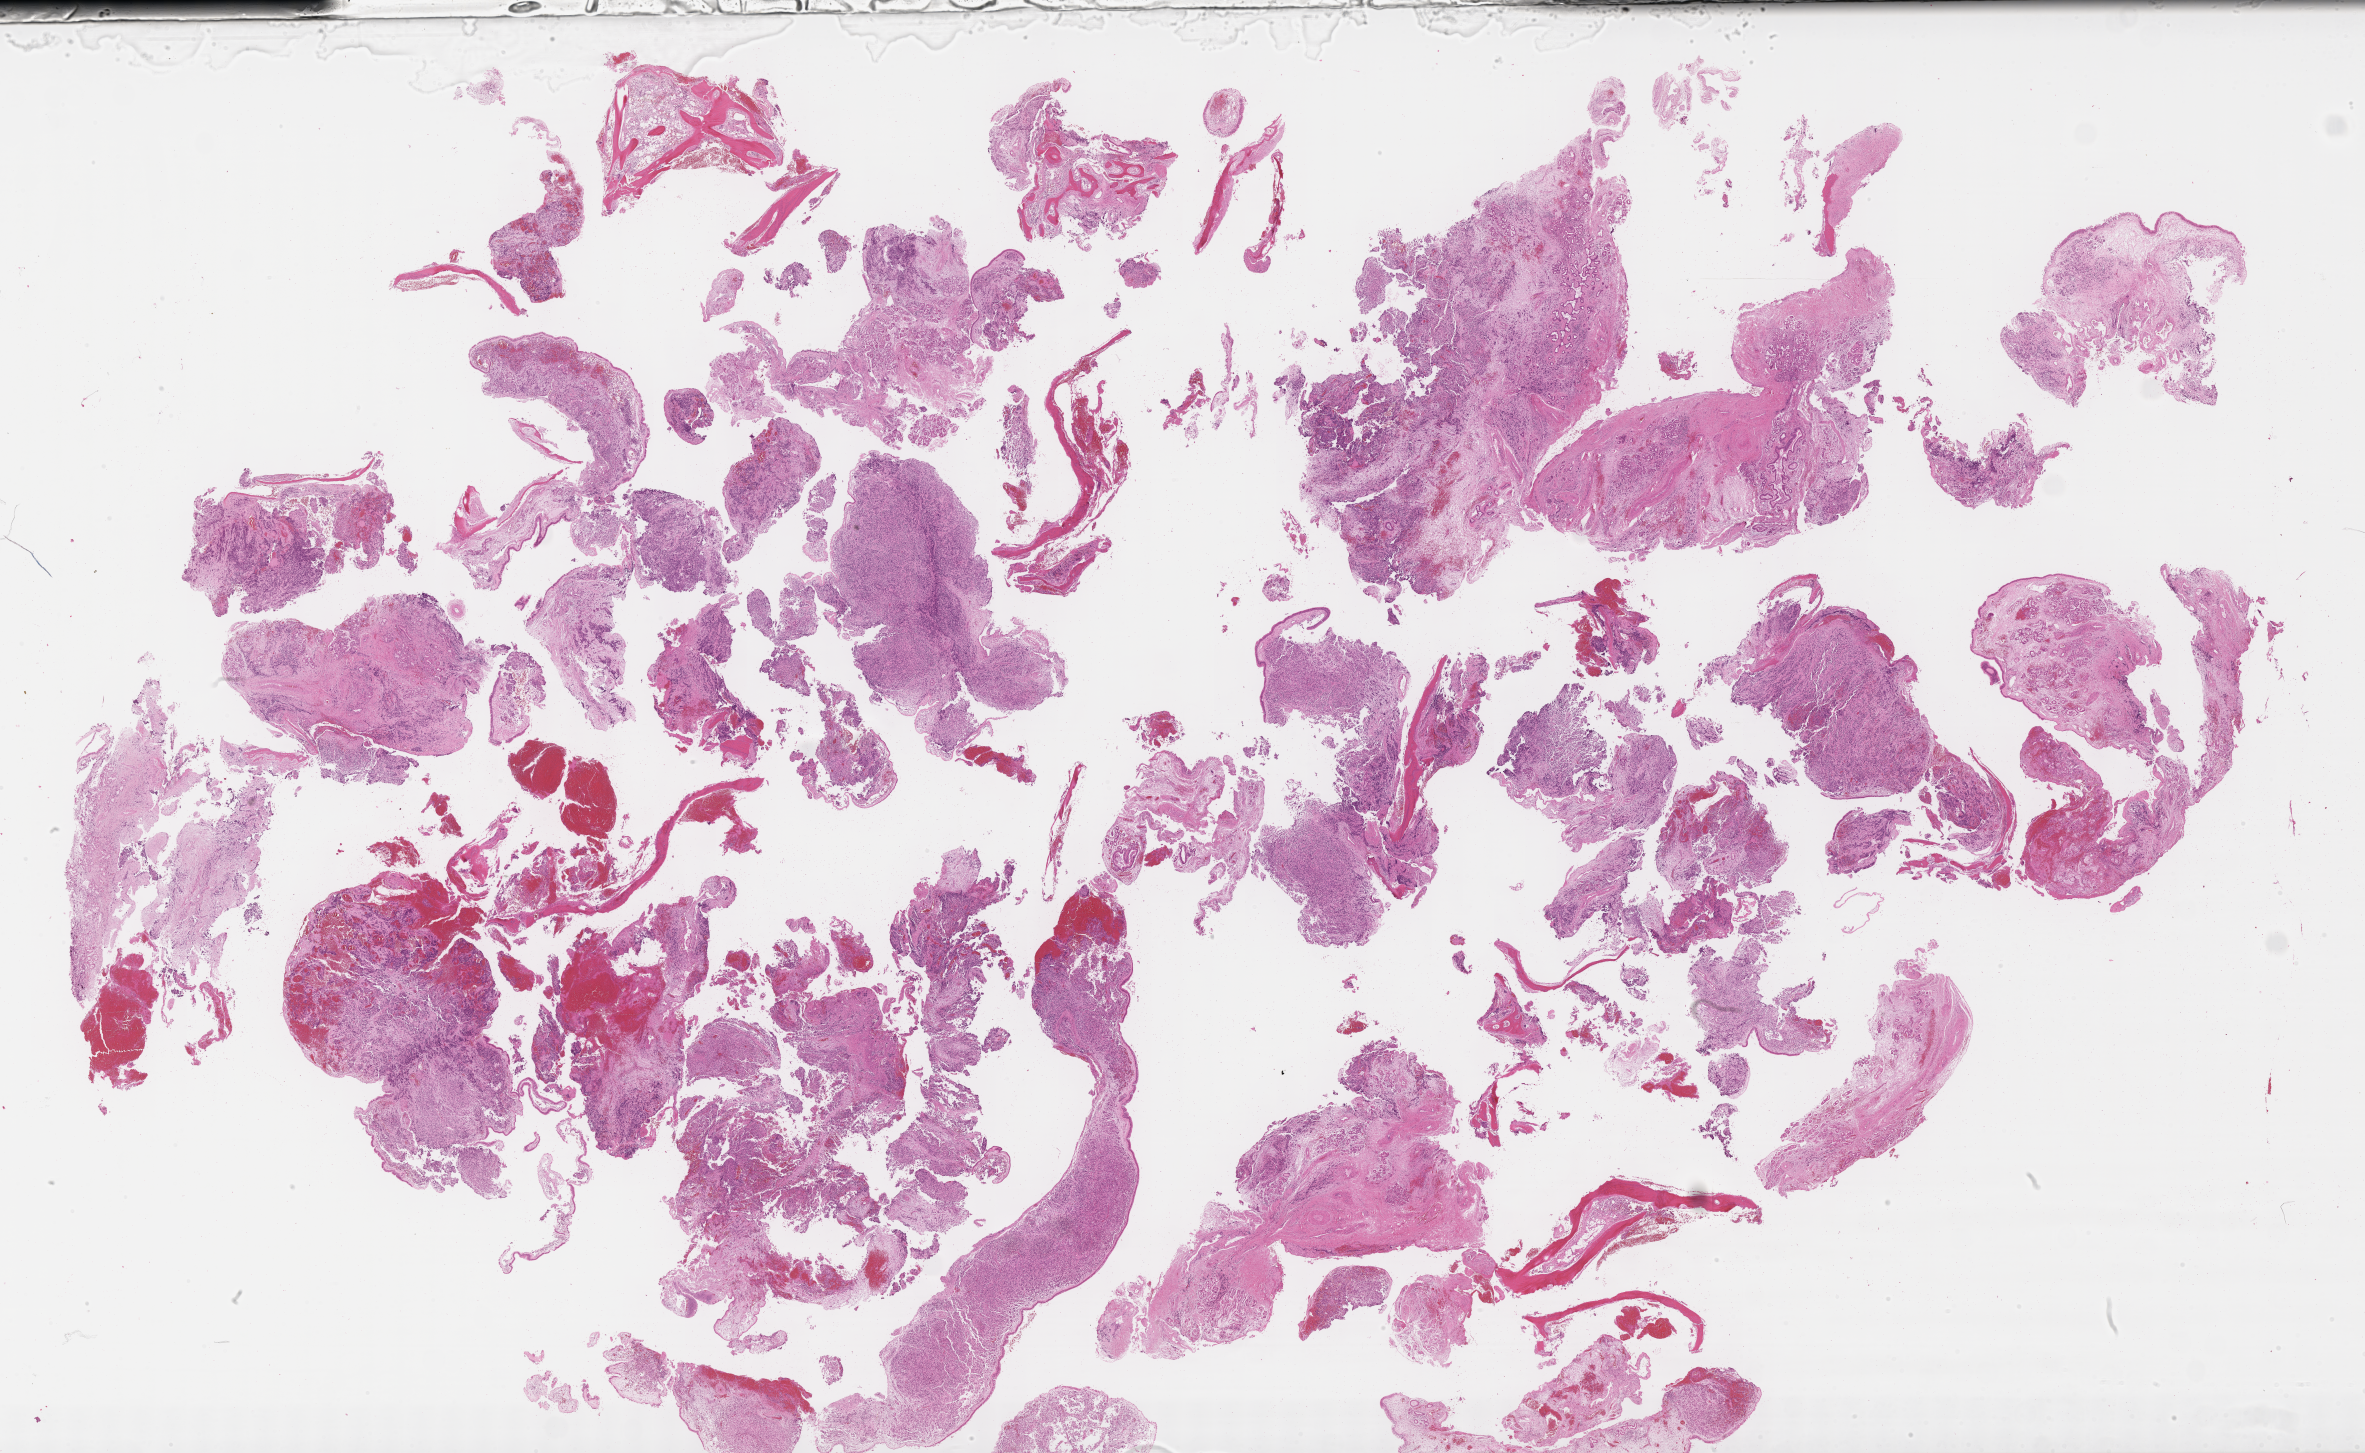
Haematoxylin and eosin whole-slide image of tumor tissue — shown as a low-resolution overview of the whole scanned area (about 38.2 x 23.5 mm); FFPE section; sample anatomic site: bone, maxilla-left (sinus). Male patient, age at diagnosis 13.1 years.
Primary site (case record): other head & neck (with PM extension). Stage (as recorded): 3. Diagnosis: rhabdomyosarcoma; histological classification: embryonal rhabdomyosarcoma.